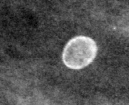
Crop from a digitized film mammogram around one marked abnormality, left breast, MLO view.
Finding: calcifications, morphology lucent center; BI-RADS assessment category 2; subtlety rating 4 on a 1 (subtle) to 5 (obvious) scale; benign without callback (not worked up further).